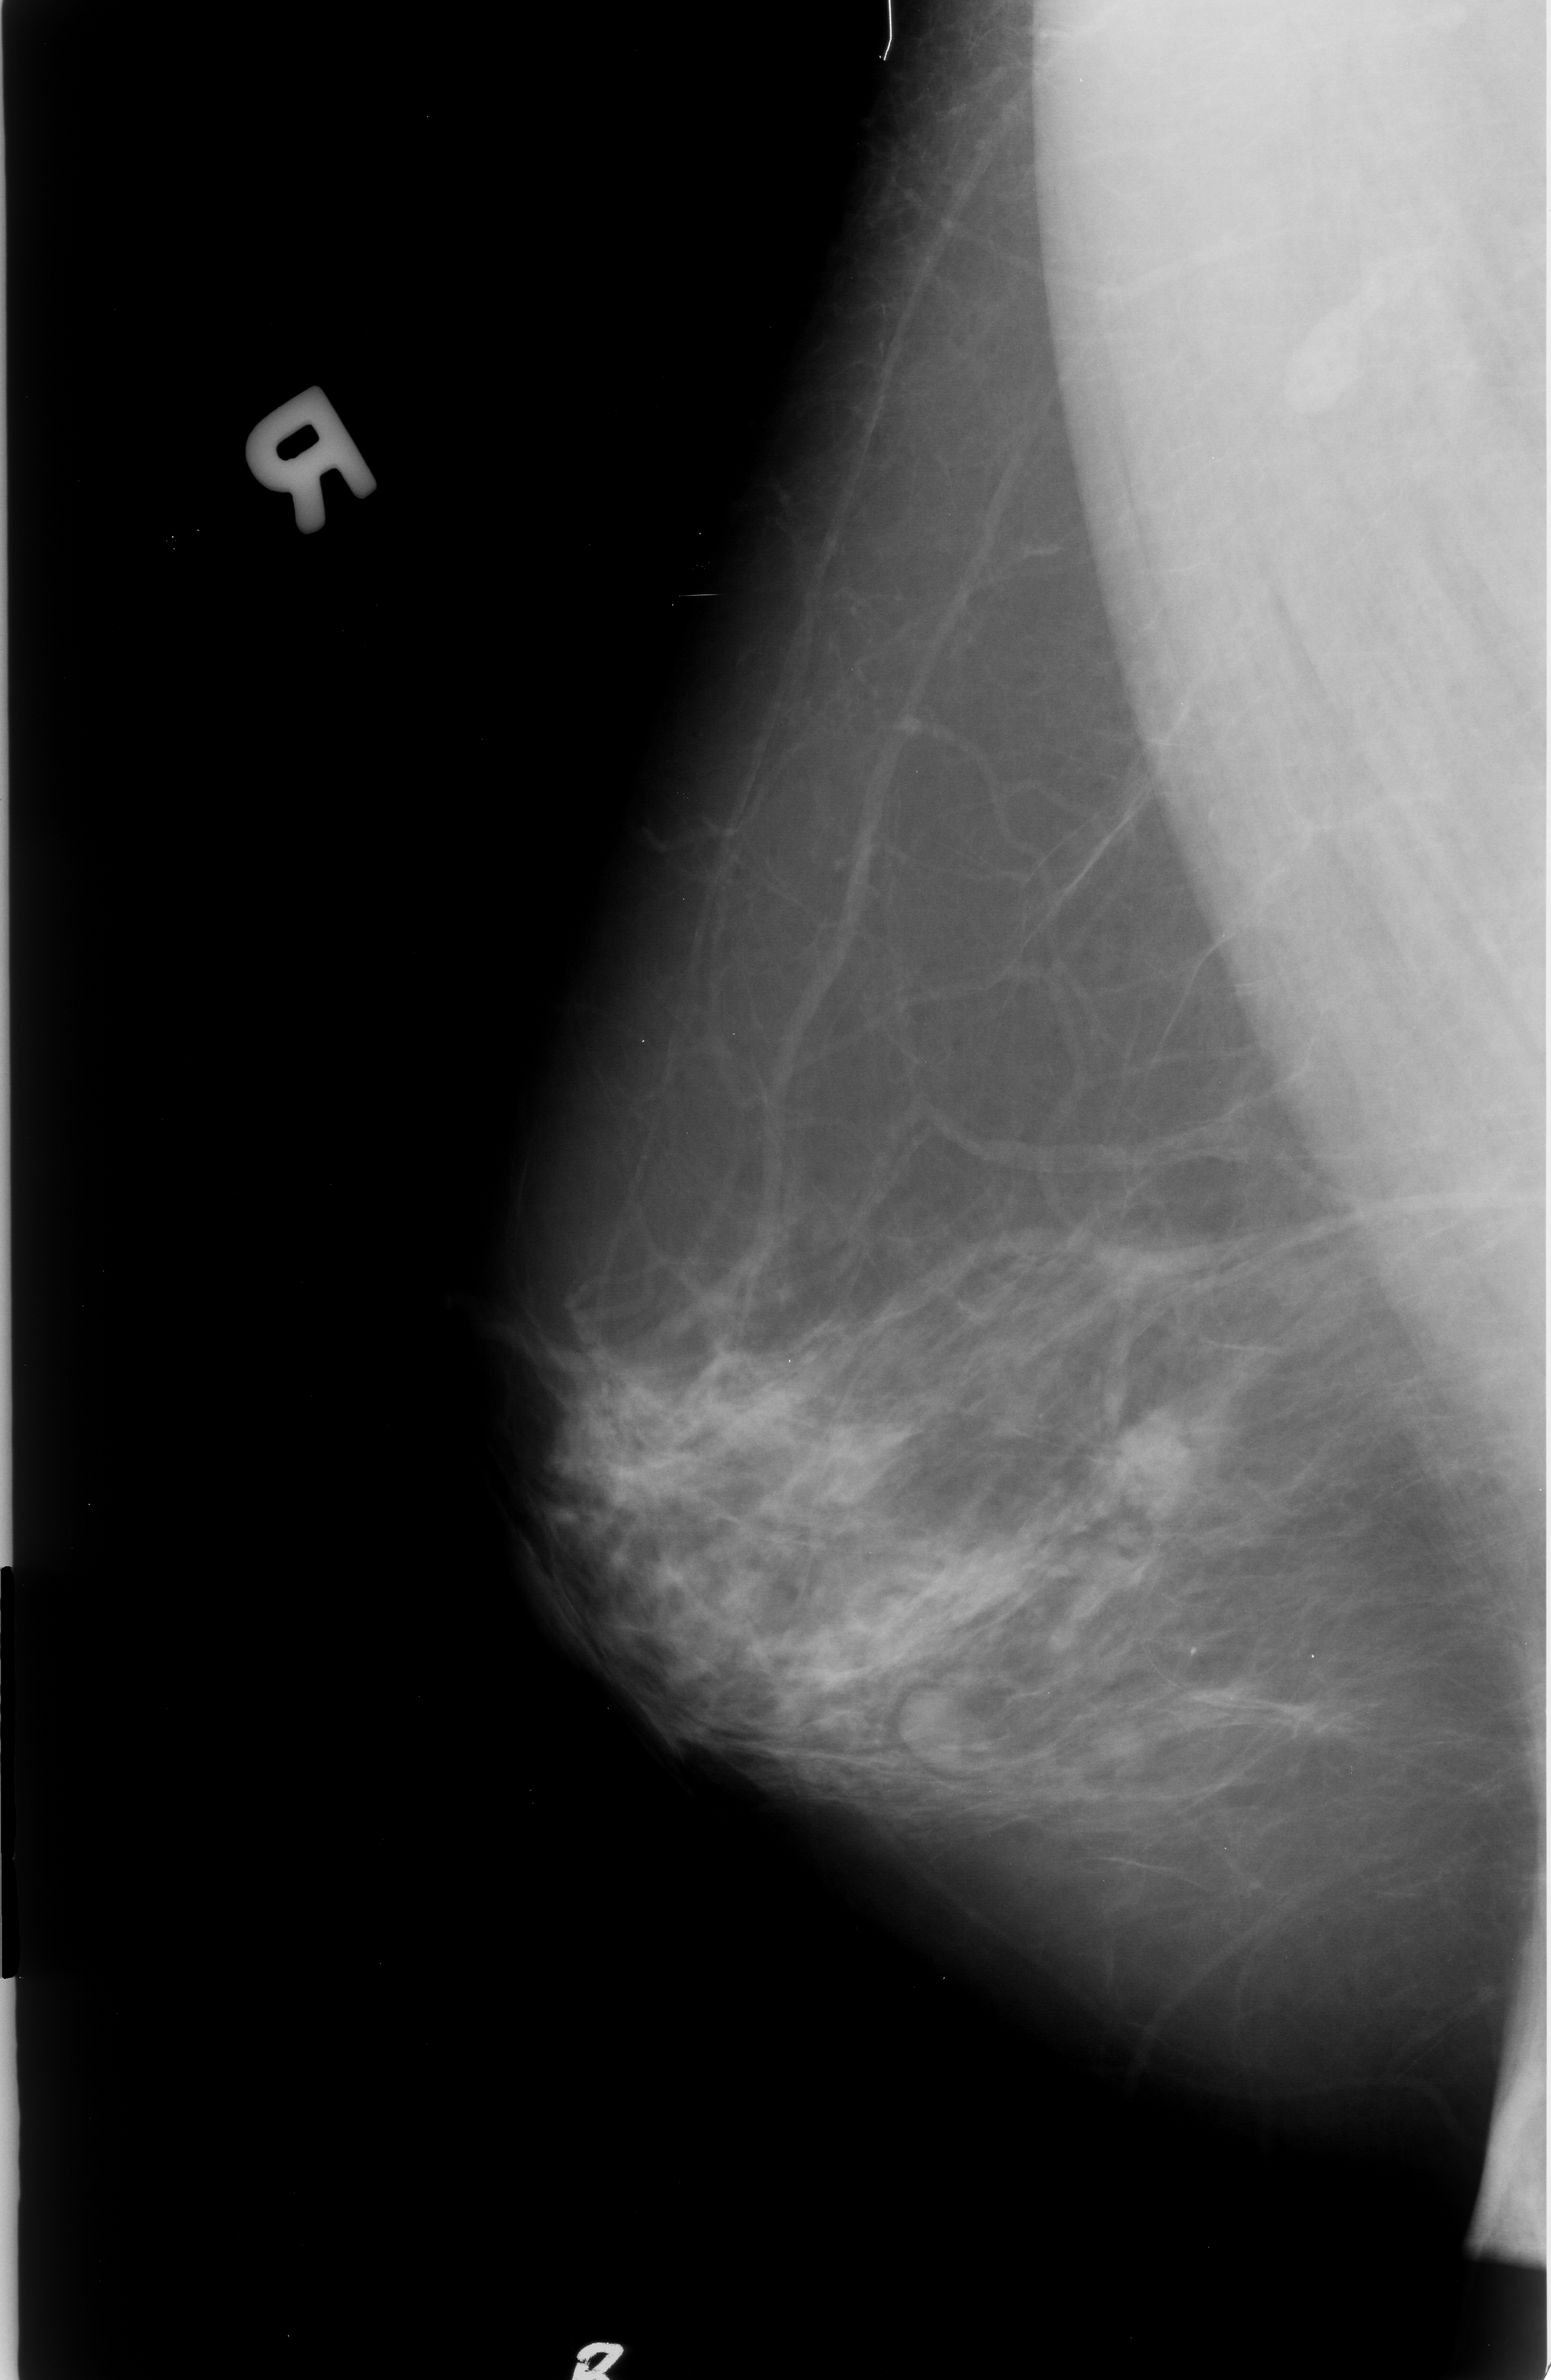
Mammogram (digitized film), right breast, mediolateral oblique (MLO) view, BI-RADS breast density category 2 (scale 1–4).
Mass, shape irregular / architectural distortion, margins microlobulated / ill defined / spiculated; BI-RADS assessment category 4; pathology result (as recorded, not read from the image): malignant.